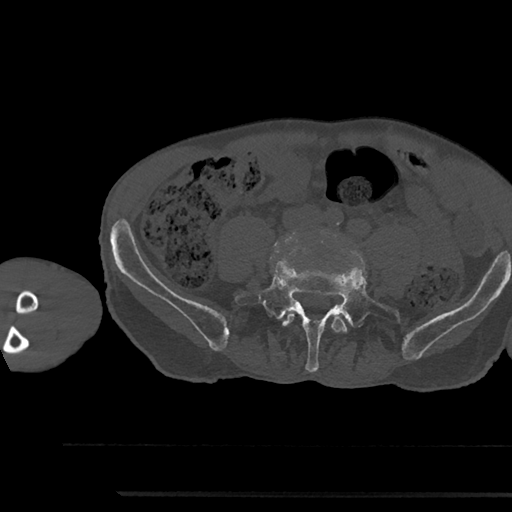
CT including the spine, one axial slice. Slice 364 of 797 in the series (ordered by position). Reconstruction kernel Br40s/3. Bone window (W 1800 / L 400 HU). 0.5 mm slice thickness. 512 × 512 image matrix, field of view 367 × 367 mm. Male patient, age 79 years. Case-level facts recorded for this patient, not image findings: primary cancer: prostate.
Structures marked on this image (semi-automatic segmentation, software-assisted and operator-edited):
- L4 vertebra: bounding box <282,312,348,333> (left, top, right, bottom; pixels)
- L5 vertebra: <234,261,401,372>